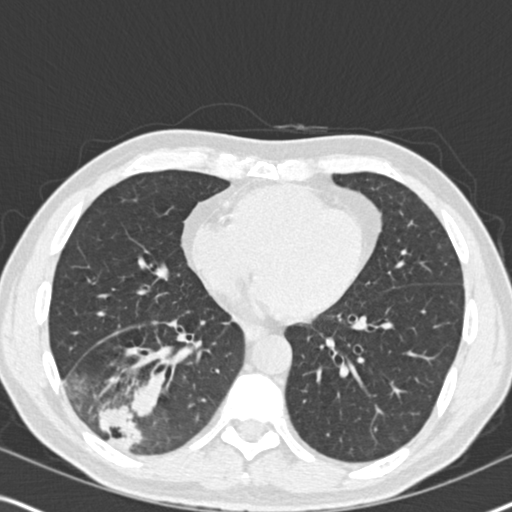
Low-dose screening chest CT, one axial slice; slice 79 of 182 in the series (ordered by position); 120 kVp; lung window (W 1500 / L -600 HU); 2 mm slice thickness; 512 × 512 image matrix, field of view 330 × 330 mm.
Structures marked on this image (manually delineated by an expert):
- lesion 1 (tumor, lower lobe of right lung): bounding box (x1, y1, x2, y2) in pixels: (98, 382, 160, 449)